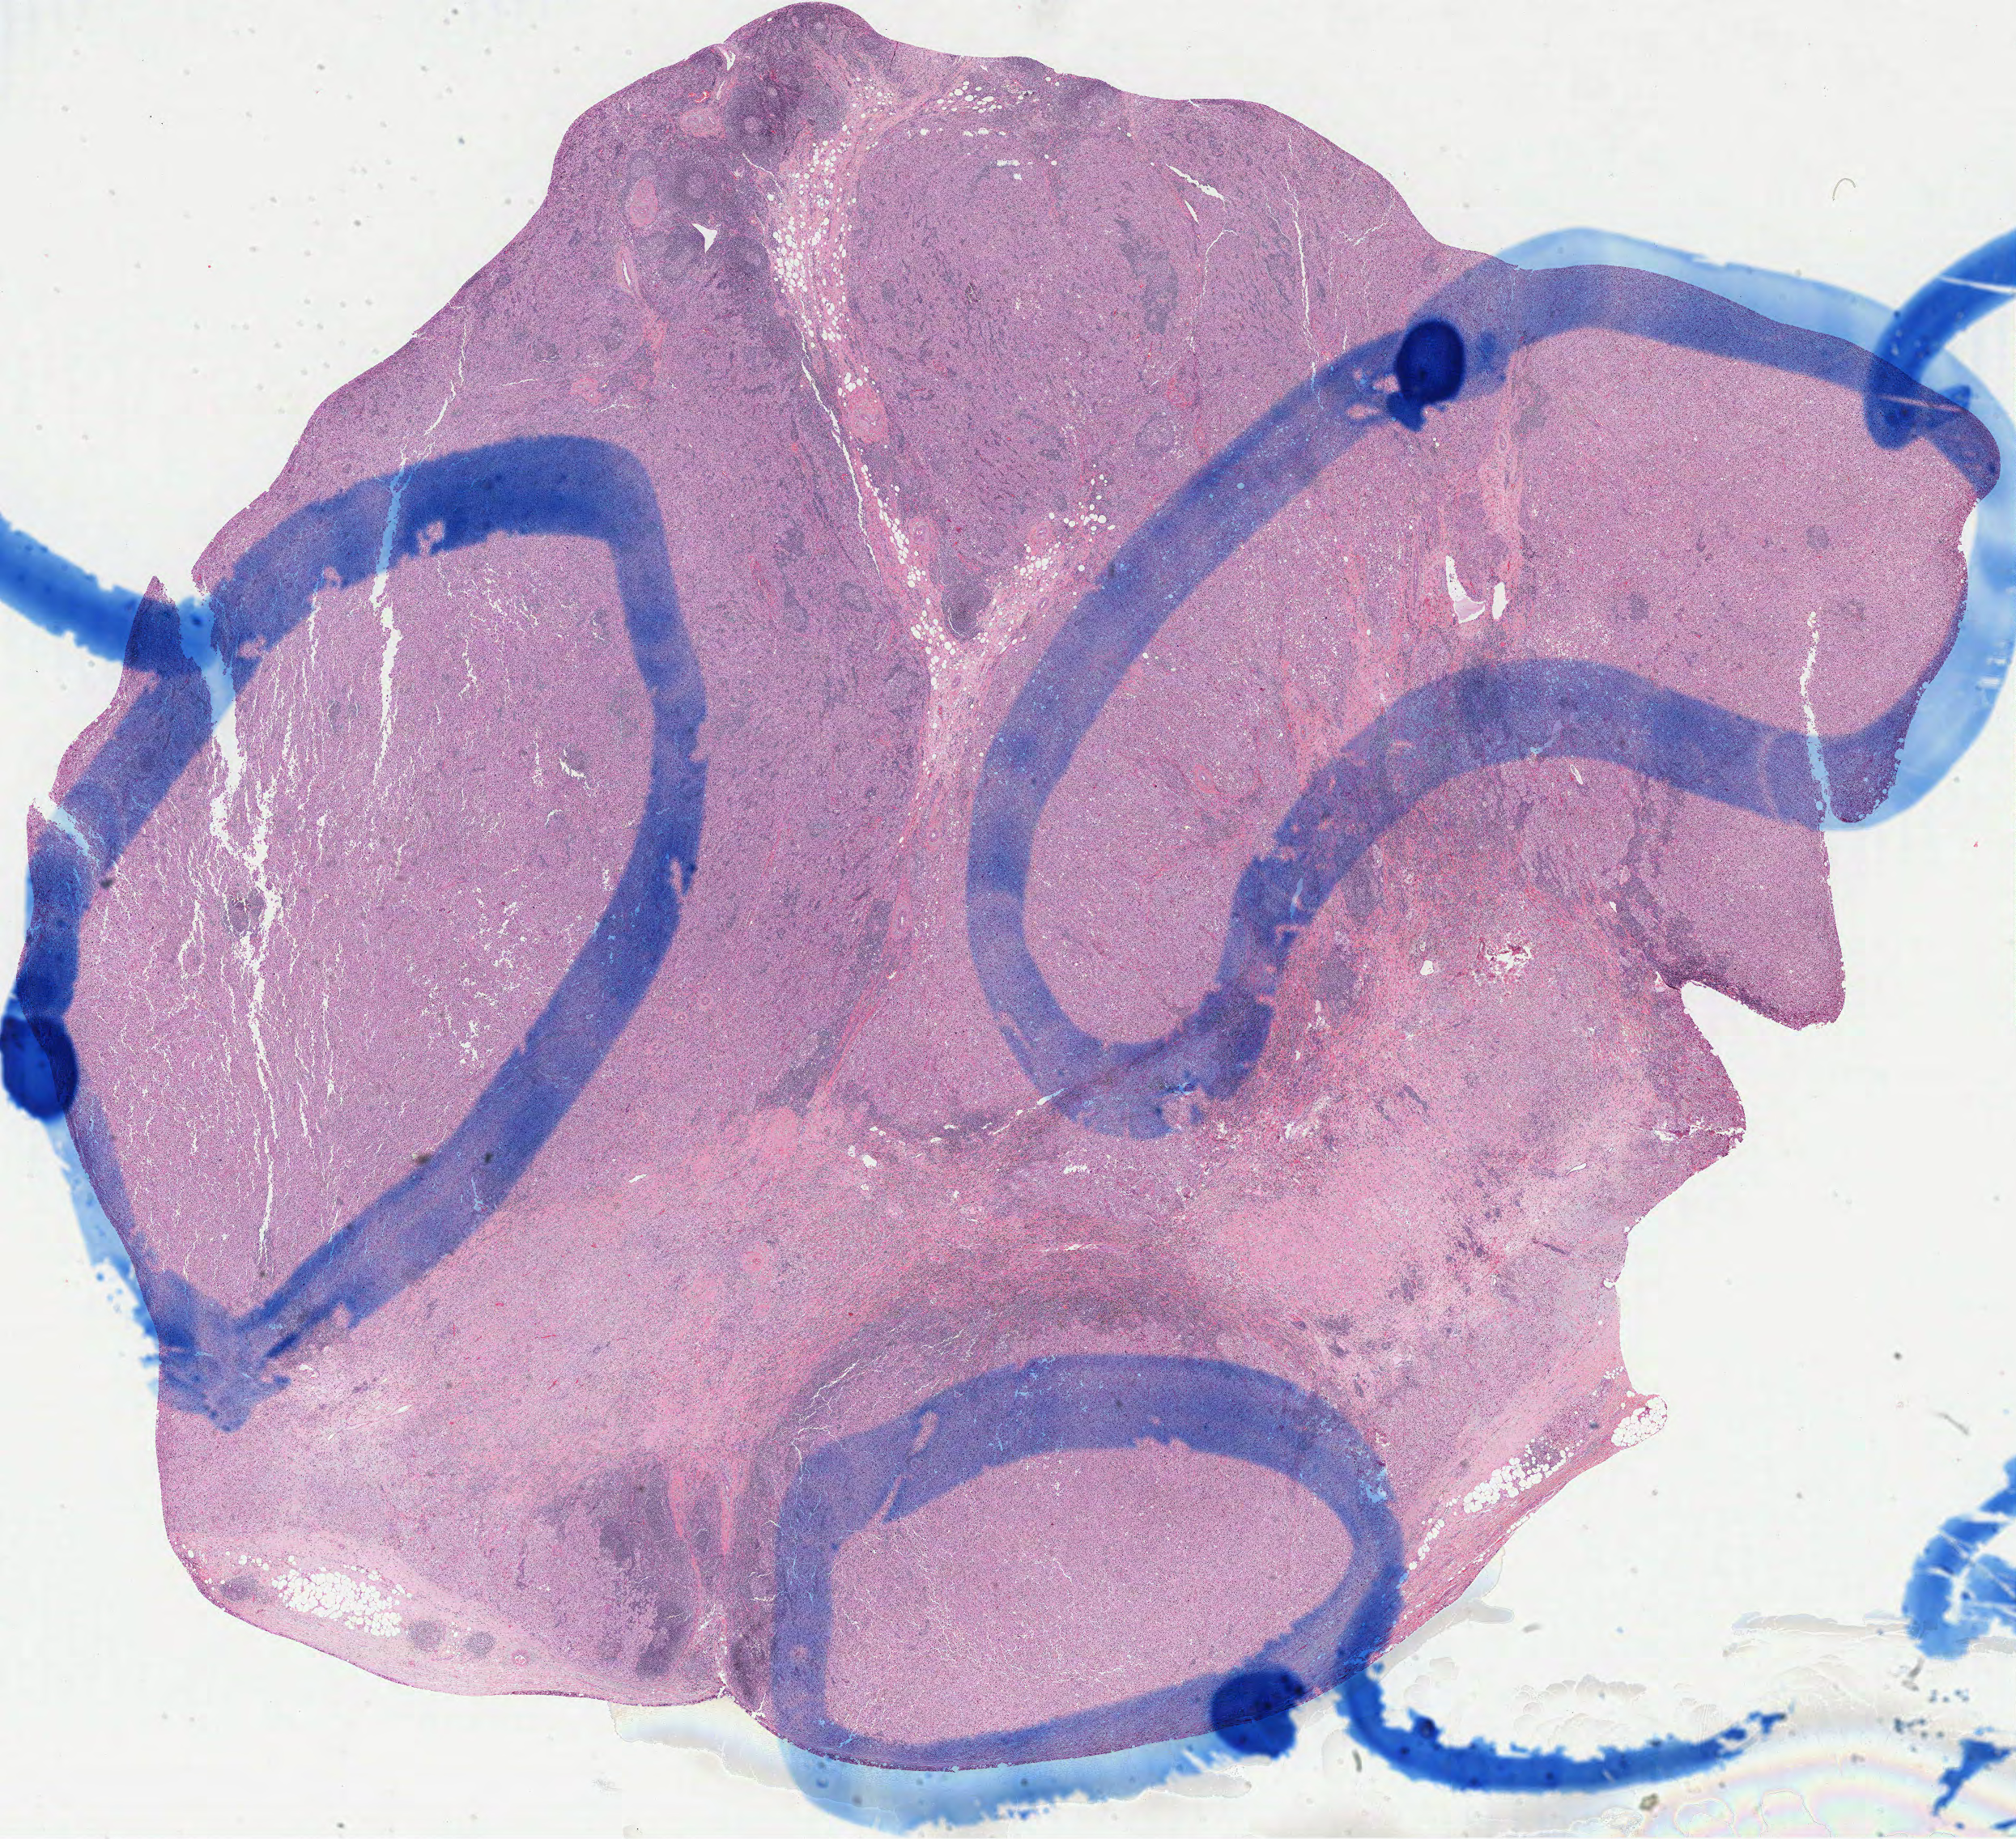
H&E whole-slide image, a low-resolution overview of the entire scanned area, about 20.0 x 18.2 mm (acquisition: 40x scan), FFPE section, metastatic tumour sample. Patient: male, age at initial diagnosis 48 years.
- this section: metastatic tumour tissue
- patient diagnosis: Malignant melanoma, NOS